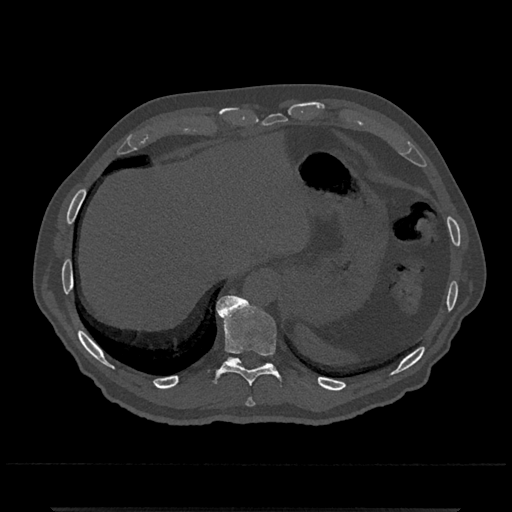
CT including the spine, one axial slice. Position 548 of 797 along the scan axis. Reconstruction kernel Br40s/3. 120 kVp. Bone window (W 1800 / L 400 HU). 0.5 mm slice thickness. 512 × 512 image matrix, field of view 393 × 393 mm. Male patient, age 67 years. From the clinical record (not read from this slice): primary cancer: prostate.
Outlined on this slice (semi-automatic segmentation, software-assisted and operator-edited):
- T10 vertebra: bounding box (x1, y1, x2, y2) in pixels: (208, 295, 279, 386)
- T11 vertebra: (227, 357, 241, 363)
- T9 vertebra: (246, 399, 255, 407)